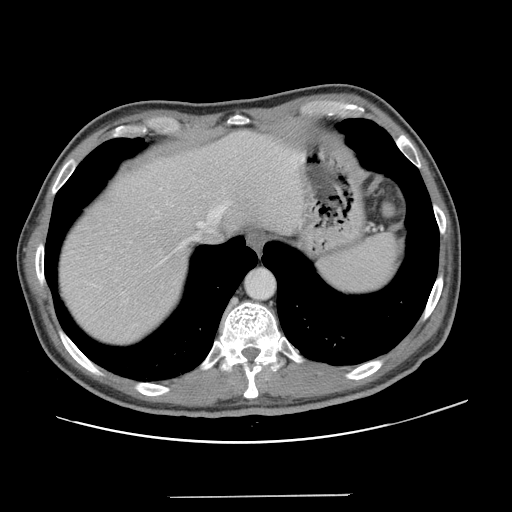
Contrast-enhanced abdominal CT, one axial slice. Slice 112 of 131 in the series (ordered by position). Intravenous contrast given. Soft-tissue window (W 400 / L 40 HU). 512 × 512 image matrix. Male patient, age 60 years. Case-level facts recorded for this patient, not image findings: diagnosis: colorectal cancer liver metastases, imaged before liver resection; multiple liver metastases: no; largest metastasis: 2.5 cm; disease in both lobes: no.
Structures marked on this image (outlined manually by an expert reader):
- hepatic veins: box from (x=154, y=204) to (x=226, y=268) px
- liver: (x=59, y=132)–(x=302, y=346)
- planned liver remnant (the part of the liver to remain after resection): (x=59, y=132)–(x=302, y=339)